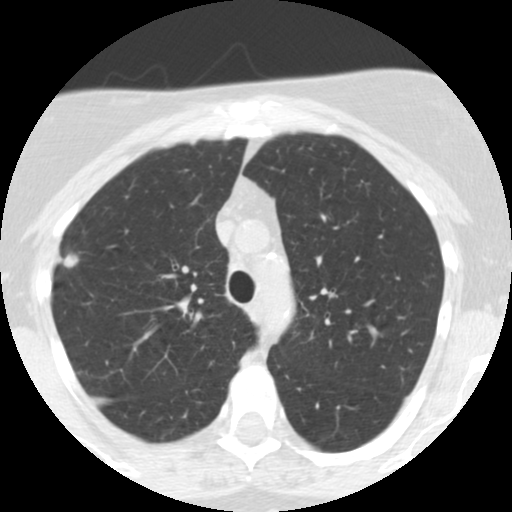
Low-dose screening chest CT, axial slice, third annual screen, lung window (W 1500 / L -600 HU), 120 kVp, slice 183 of 248 in the series, 512 × 512 image matrix, field of view 287 × 287 mm. Female participant, aged 55 years at enrolment. Current smoker at enrolment.
Expert reader's lesion annotation, box from (x=49, y=241) to (x=93, y=282) px. Screening reader's record for this exam (one nodule recorded; not confirmed to be the boxed lesion): non-calcified nodule or mass ≥4 mm, right upper lobe, 10 × 10 mm, poorly defined margins, soft tissue attenuation, pre-existing on the prior screen: yes; interval growth: yes. Later outcome: lung cancer diagnosed 145 days after this screen — bronchiolo-alveolar adenocarcinoma, NOS, right upper lobe, moderately differentiated (G2), stage IIA (AJCC 6th edition), 13 mm at pathology.